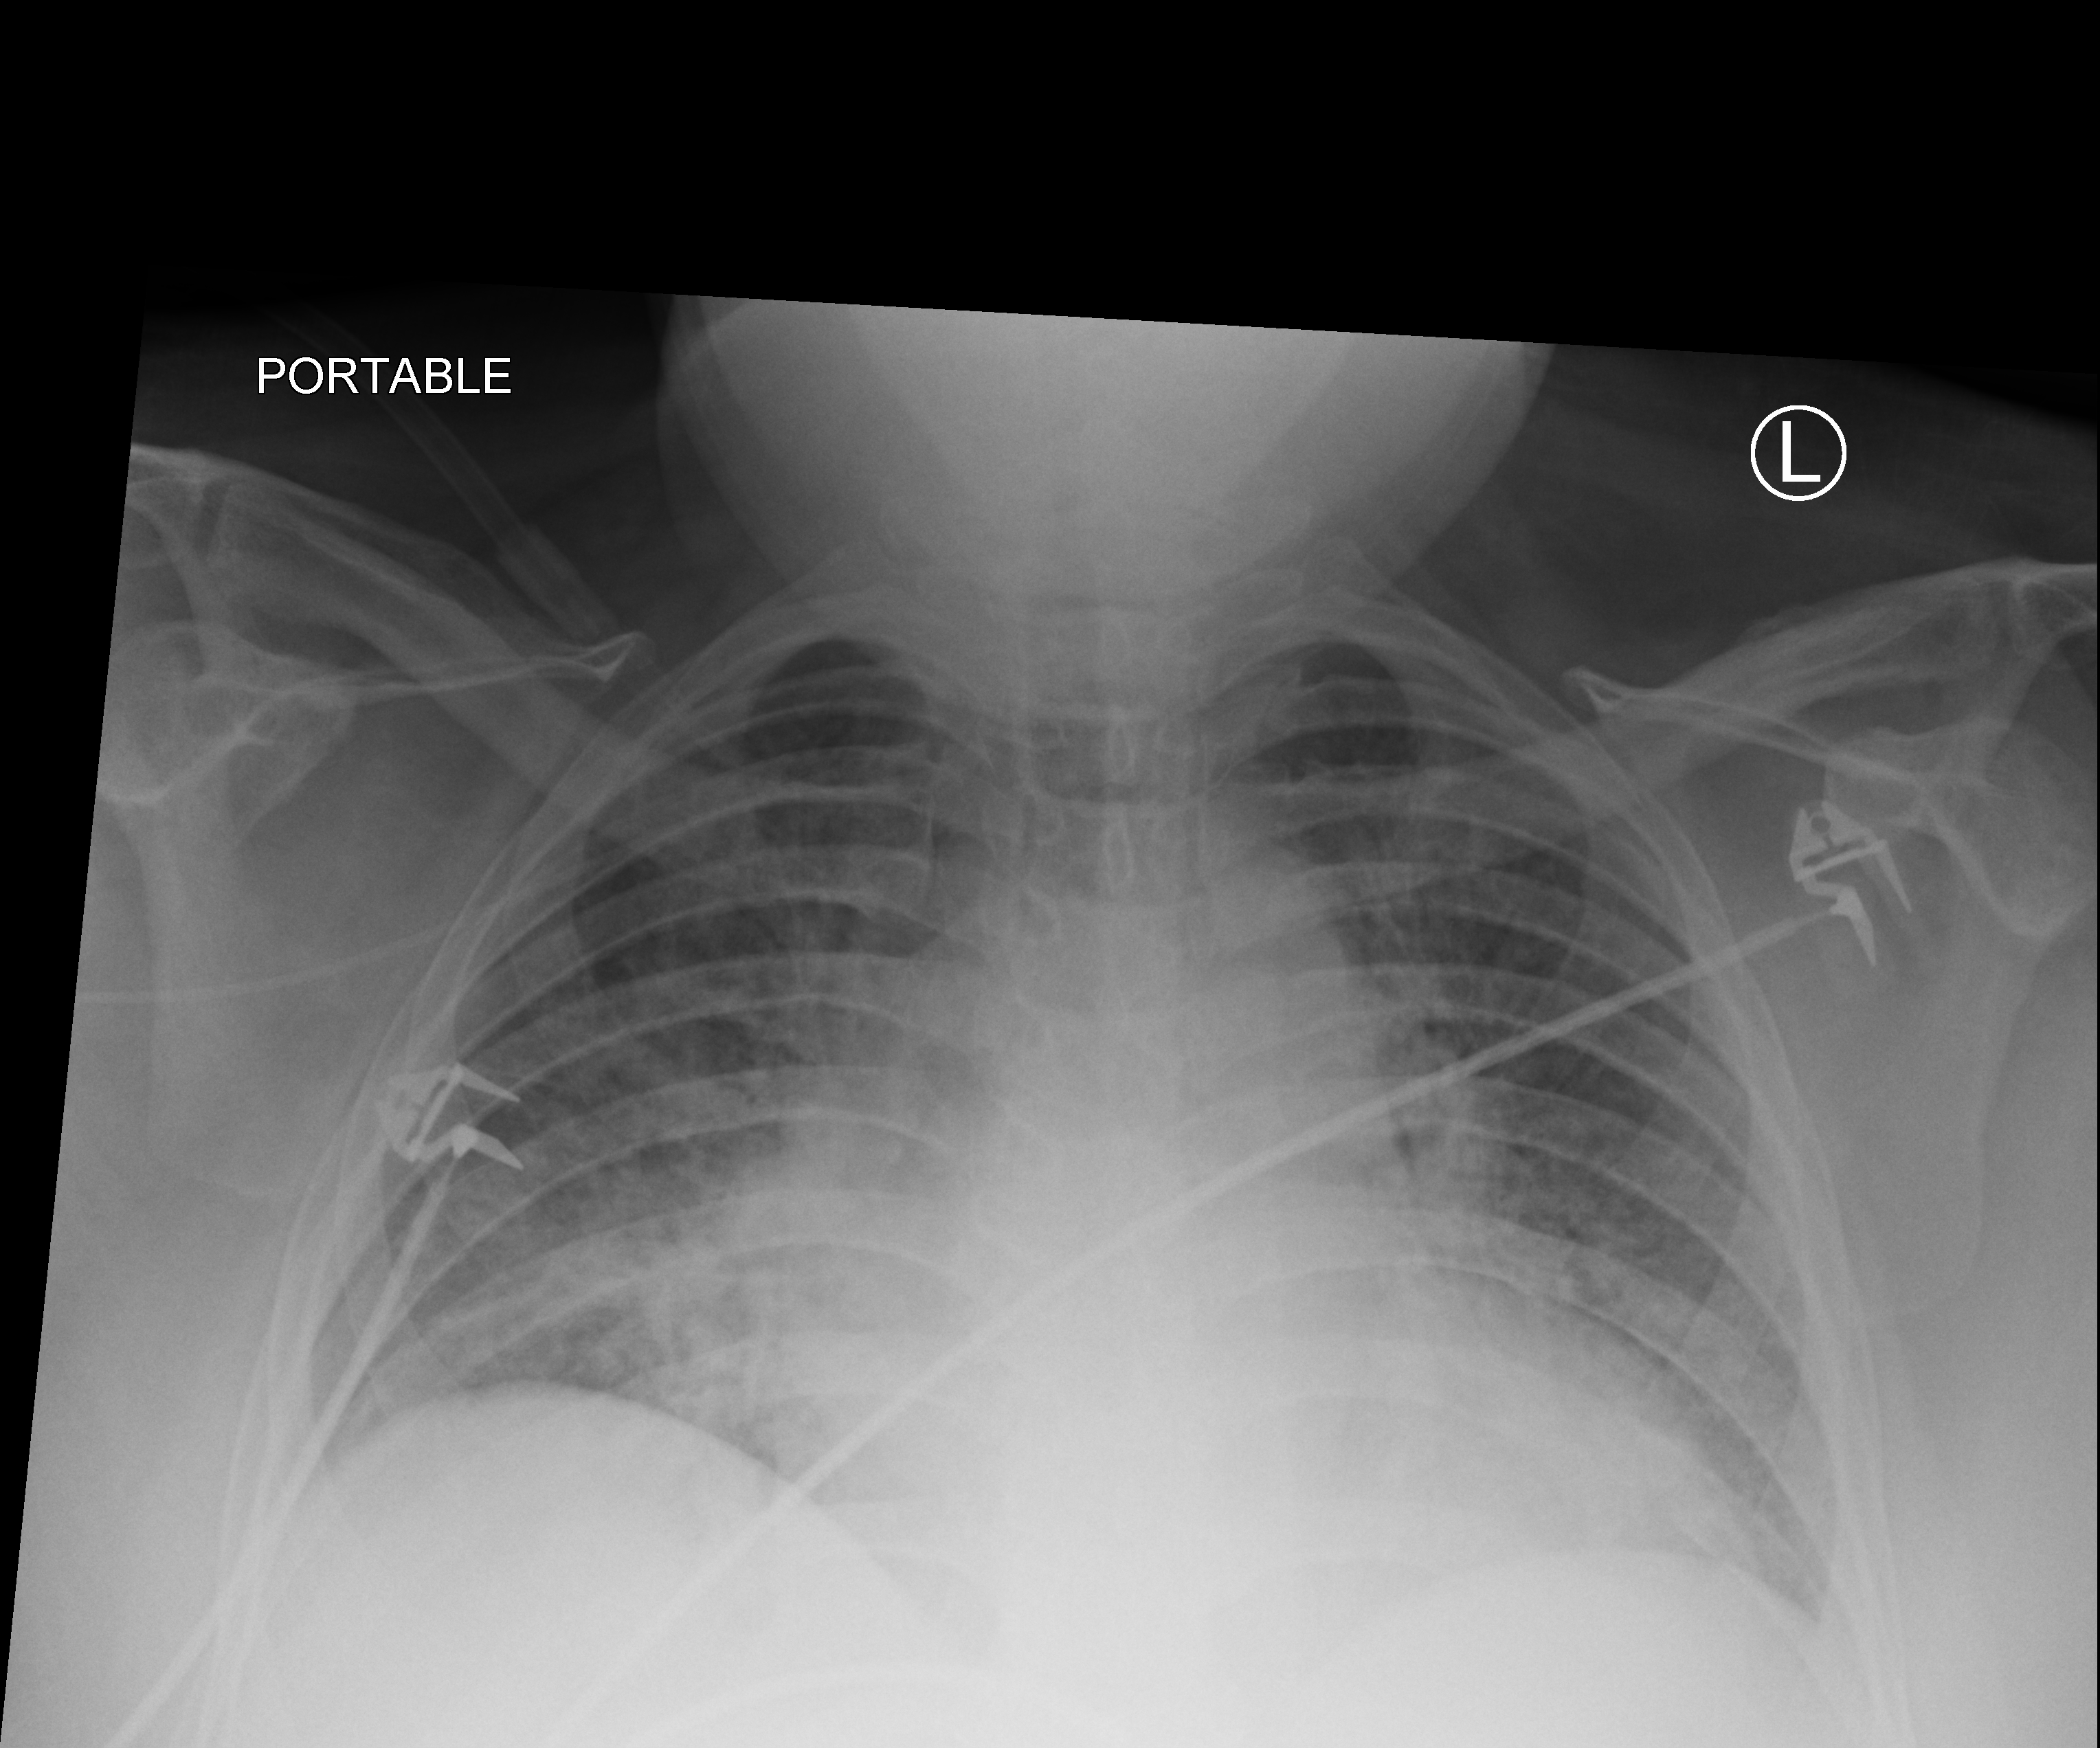
Bedside chest radiograph (computed radiography); anteroposterior (AP) projection. Patient hospitalised with COVID-19; male, aged 18–59 years.
Admission-level facts for this patient (not findings on this image; timing relative to this image not recorded): mechanically ventilated during this hospital stay: yes; admitted to intensive care during this hospital stay: yes.